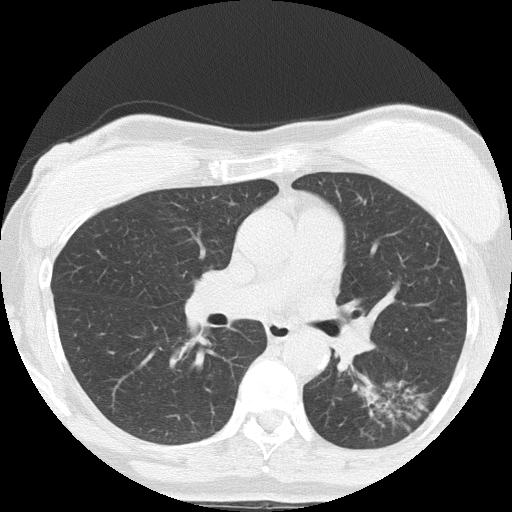
Chest CT (low-dose screening protocol), one axial image; third annual screen; lung window (W 1500 / L -600 HU); 2 mm slice thickness; slice 68 of 152 in the series. Female participant, aged 64 years at enrolment.
- Expert reader's lesion annotation, bounding box <363,369,452,444> (left, top, right, bottom; pixels).
- The screening reader recorded 3 non-calcified nodules or masses ≥4 mm on this exam (right upper lobe, left lower lobe, right middle lobe); which of them this box marks is not recorded.
- Later outcome: lung cancer diagnosed 212 days after this screen — adenocarcinoma, NOS, left lower lobe, moderately differentiated (G2), stage IA (AJCC 6th edition), 17 mm at pathology.